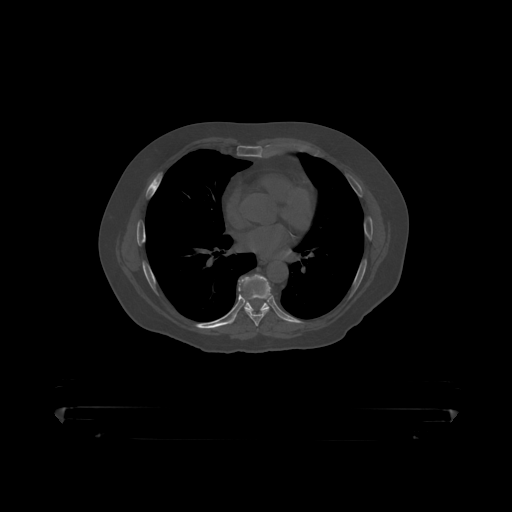
CT including the spine, one axial slice; position 270 of 390 along the scan axis; reconstruction kernel STANDARD; 120 kVp; bone window (W 1800 / L 400 HU); 512 × 512 image matrix. Patient: male, 60 years. From the clinical record (not read from this slice): primary cancer: prostate.
Outlined on this slice (semi-automatically segmented with operator editing):
- T7 vertebra: bounding box (x1, y1, x2, y2) in pixels: (239, 275, 271, 319)
- T8 vertebra: (239, 275, 271, 312)